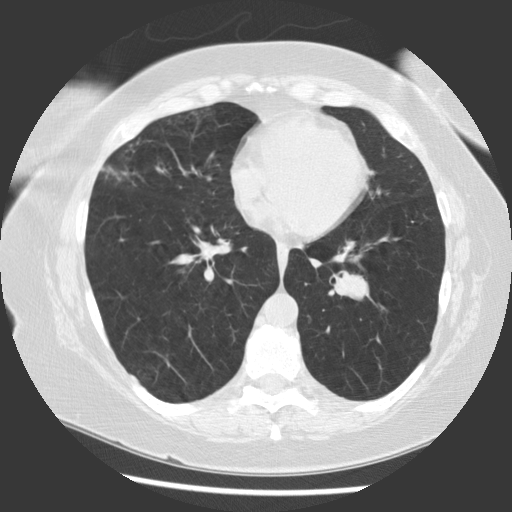
Low-dose screening chest CT, one axial slice; position 57 of 130 along the scan axis; reconstruction kernel STANDARD; 120 kVp; lung window (W 1500 / L -600 HU); 512 × 512 image matrix, field of view 340 × 340 mm.
Outlined on this slice (manually delineated by an expert):
- lesion 1 (tumor, hilum of left lung): box from (x=342, y=275) to (x=369, y=299) px